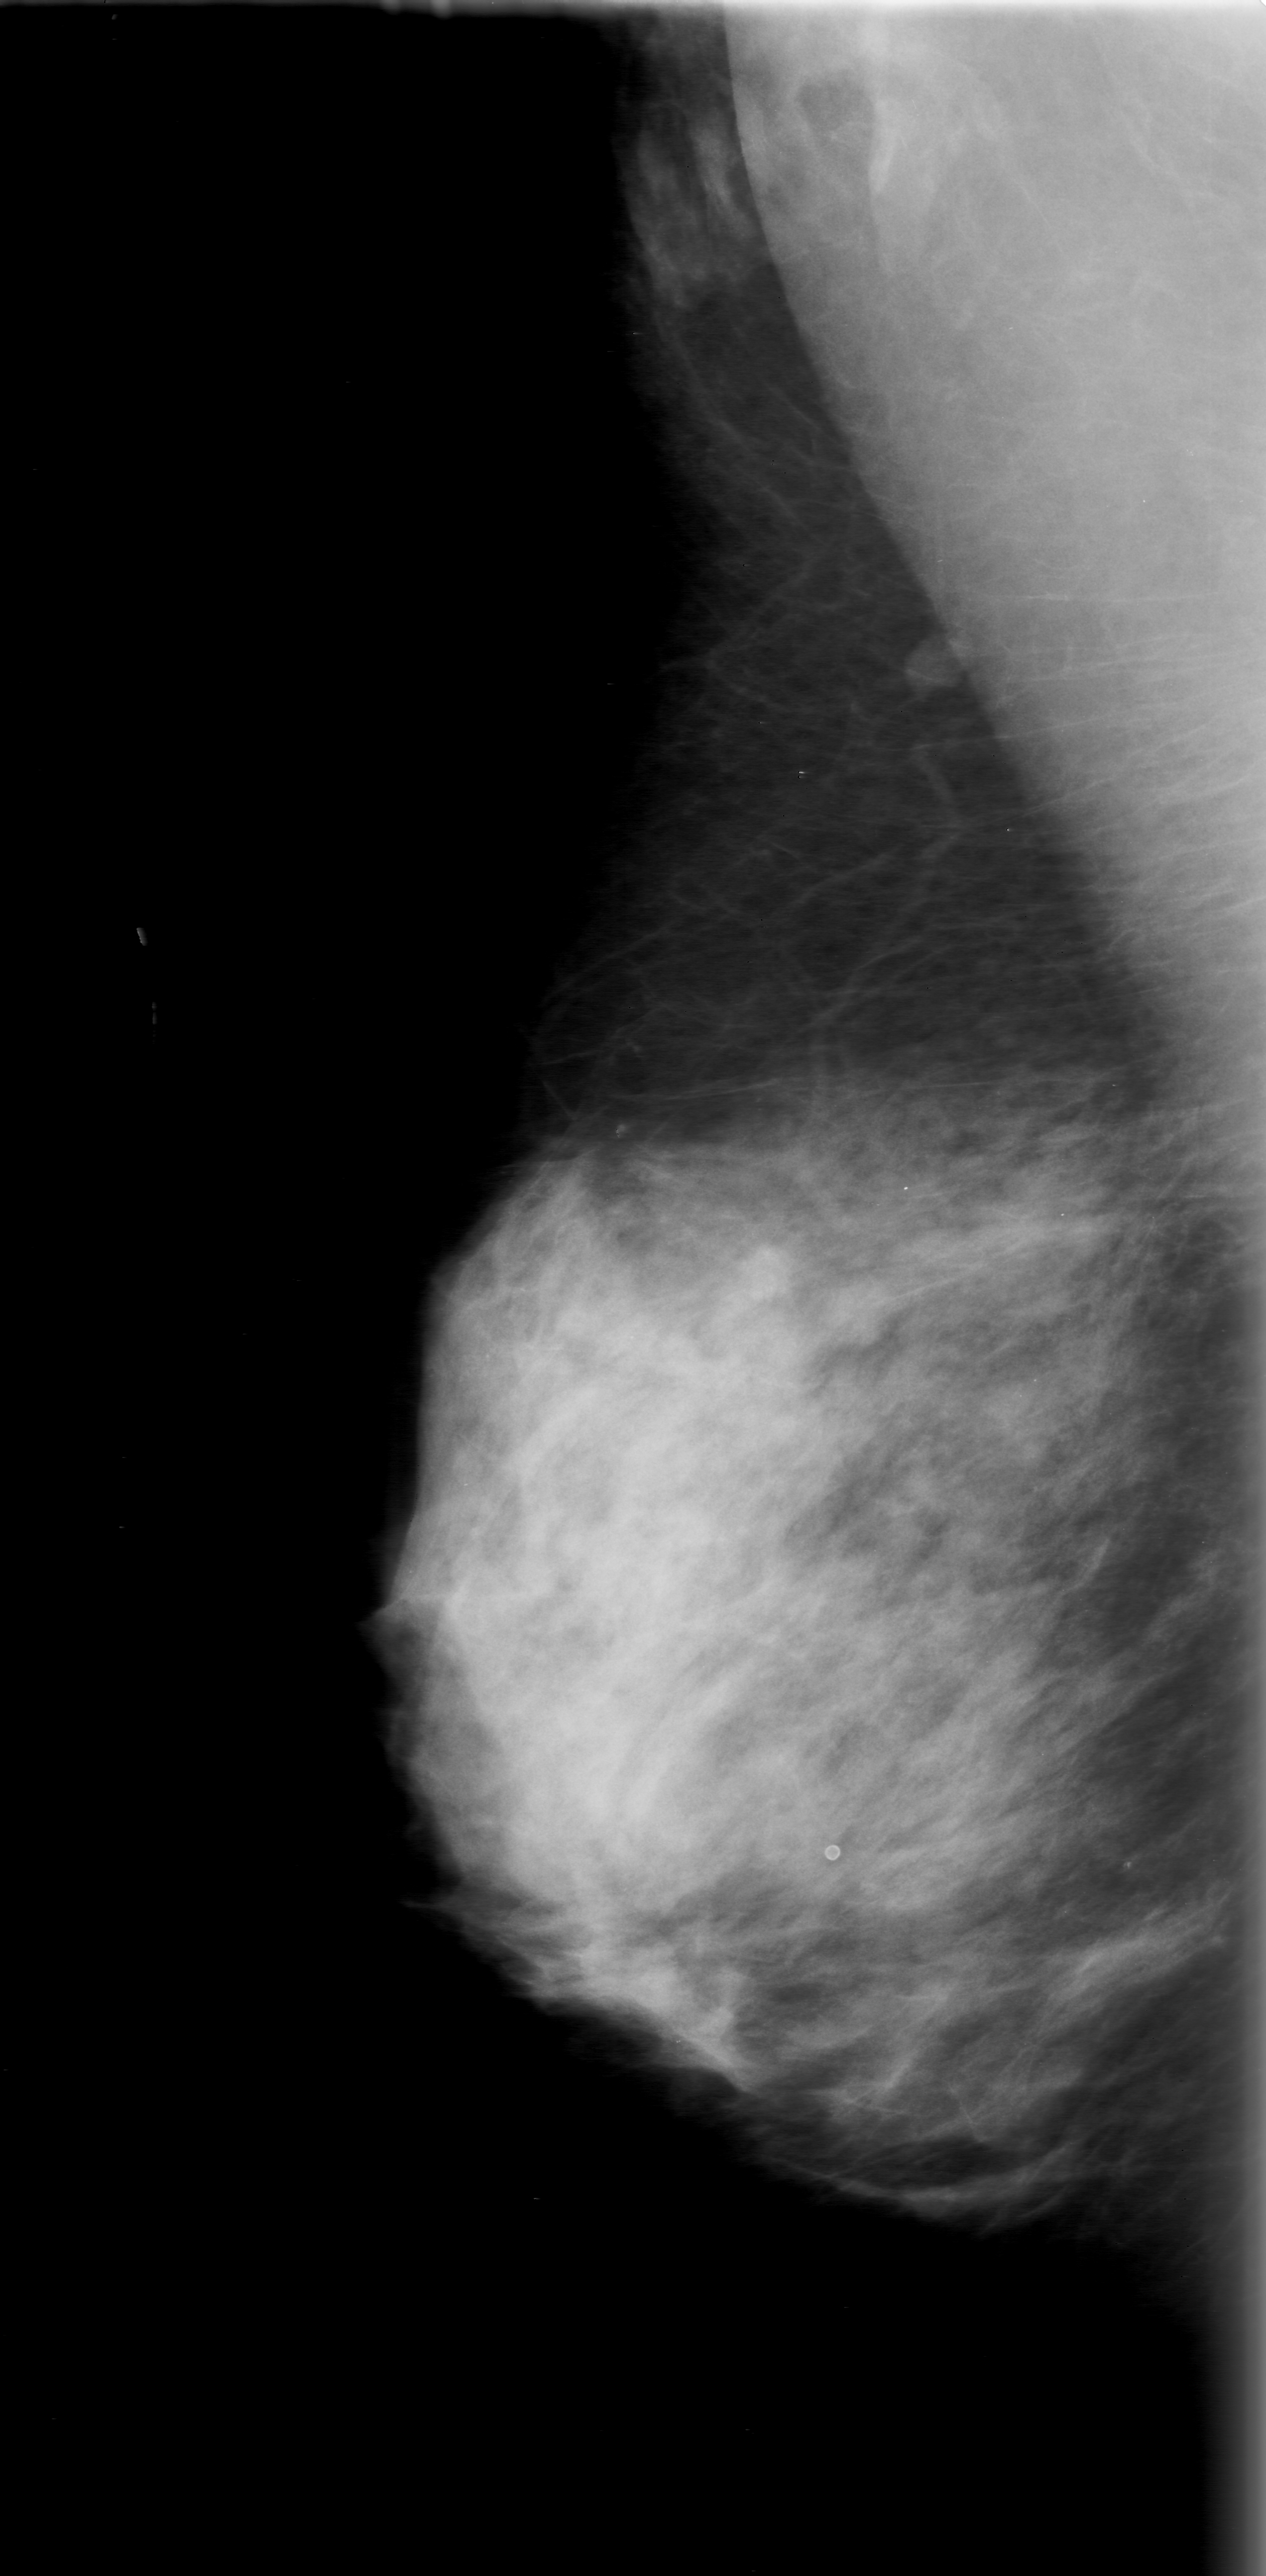
Digitized screen-film mammogram; right breast; MLO view; breast composition: extremely dense (BI-RADS density category 4 of 4).
Abnormality record for this image: mass, shape lobulated, margins obscured; BI-RADS assessment category 0 (incomplete: needs additional imaging); subtlety rating 3 on a 1 (subtle) to 5 (obvious) scale; pathology (as recorded): benign.